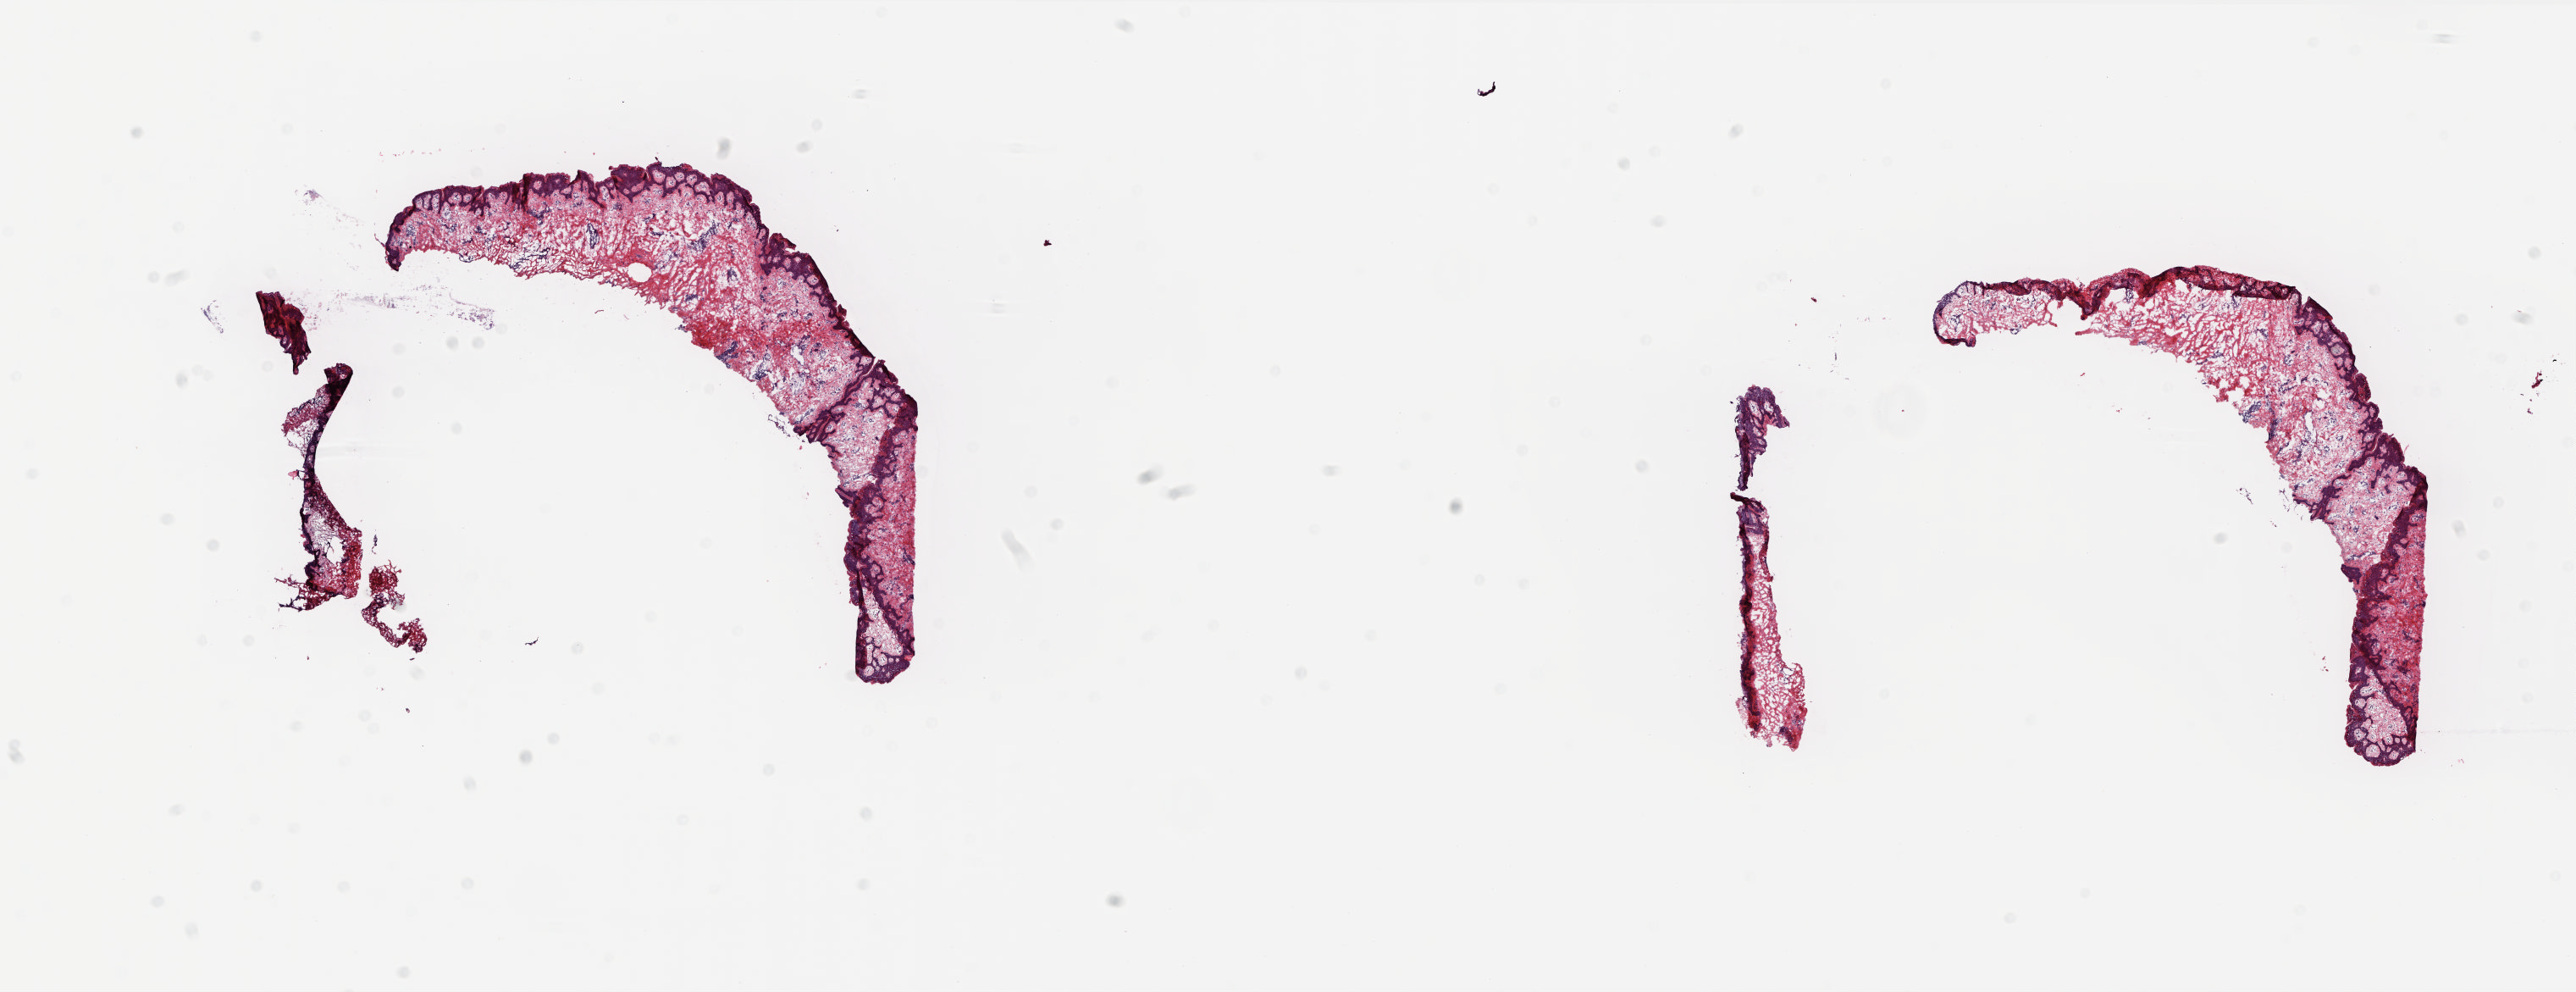
H&E-stained whole-slide image, low-resolution overview of the scanned area, about 24.5 x 9.4 mm; frozen section from the top of the tissue portion; sample: solid tissue normal (non-tumour tissue), connective, subcutaneous and other soft tissues. Female, age 53 years at initial diagnosis. Pathologist review of this section (percent, as recorded): tumour cells 0%, tumour nuclei 0%, normal cells 100%, stromal cells 0%, necrosis 0%. Infiltration values recorded for this section: lymphocyte infiltration 3%, monocyte infiltration 0%, neutrophil infiltration 0%.
This section: solid tissue normal sample (biorepository sample class). Patient diagnosis: Leiomyosarcoma, NOS (connective, subcutaneous and other soft tissues, NOS).